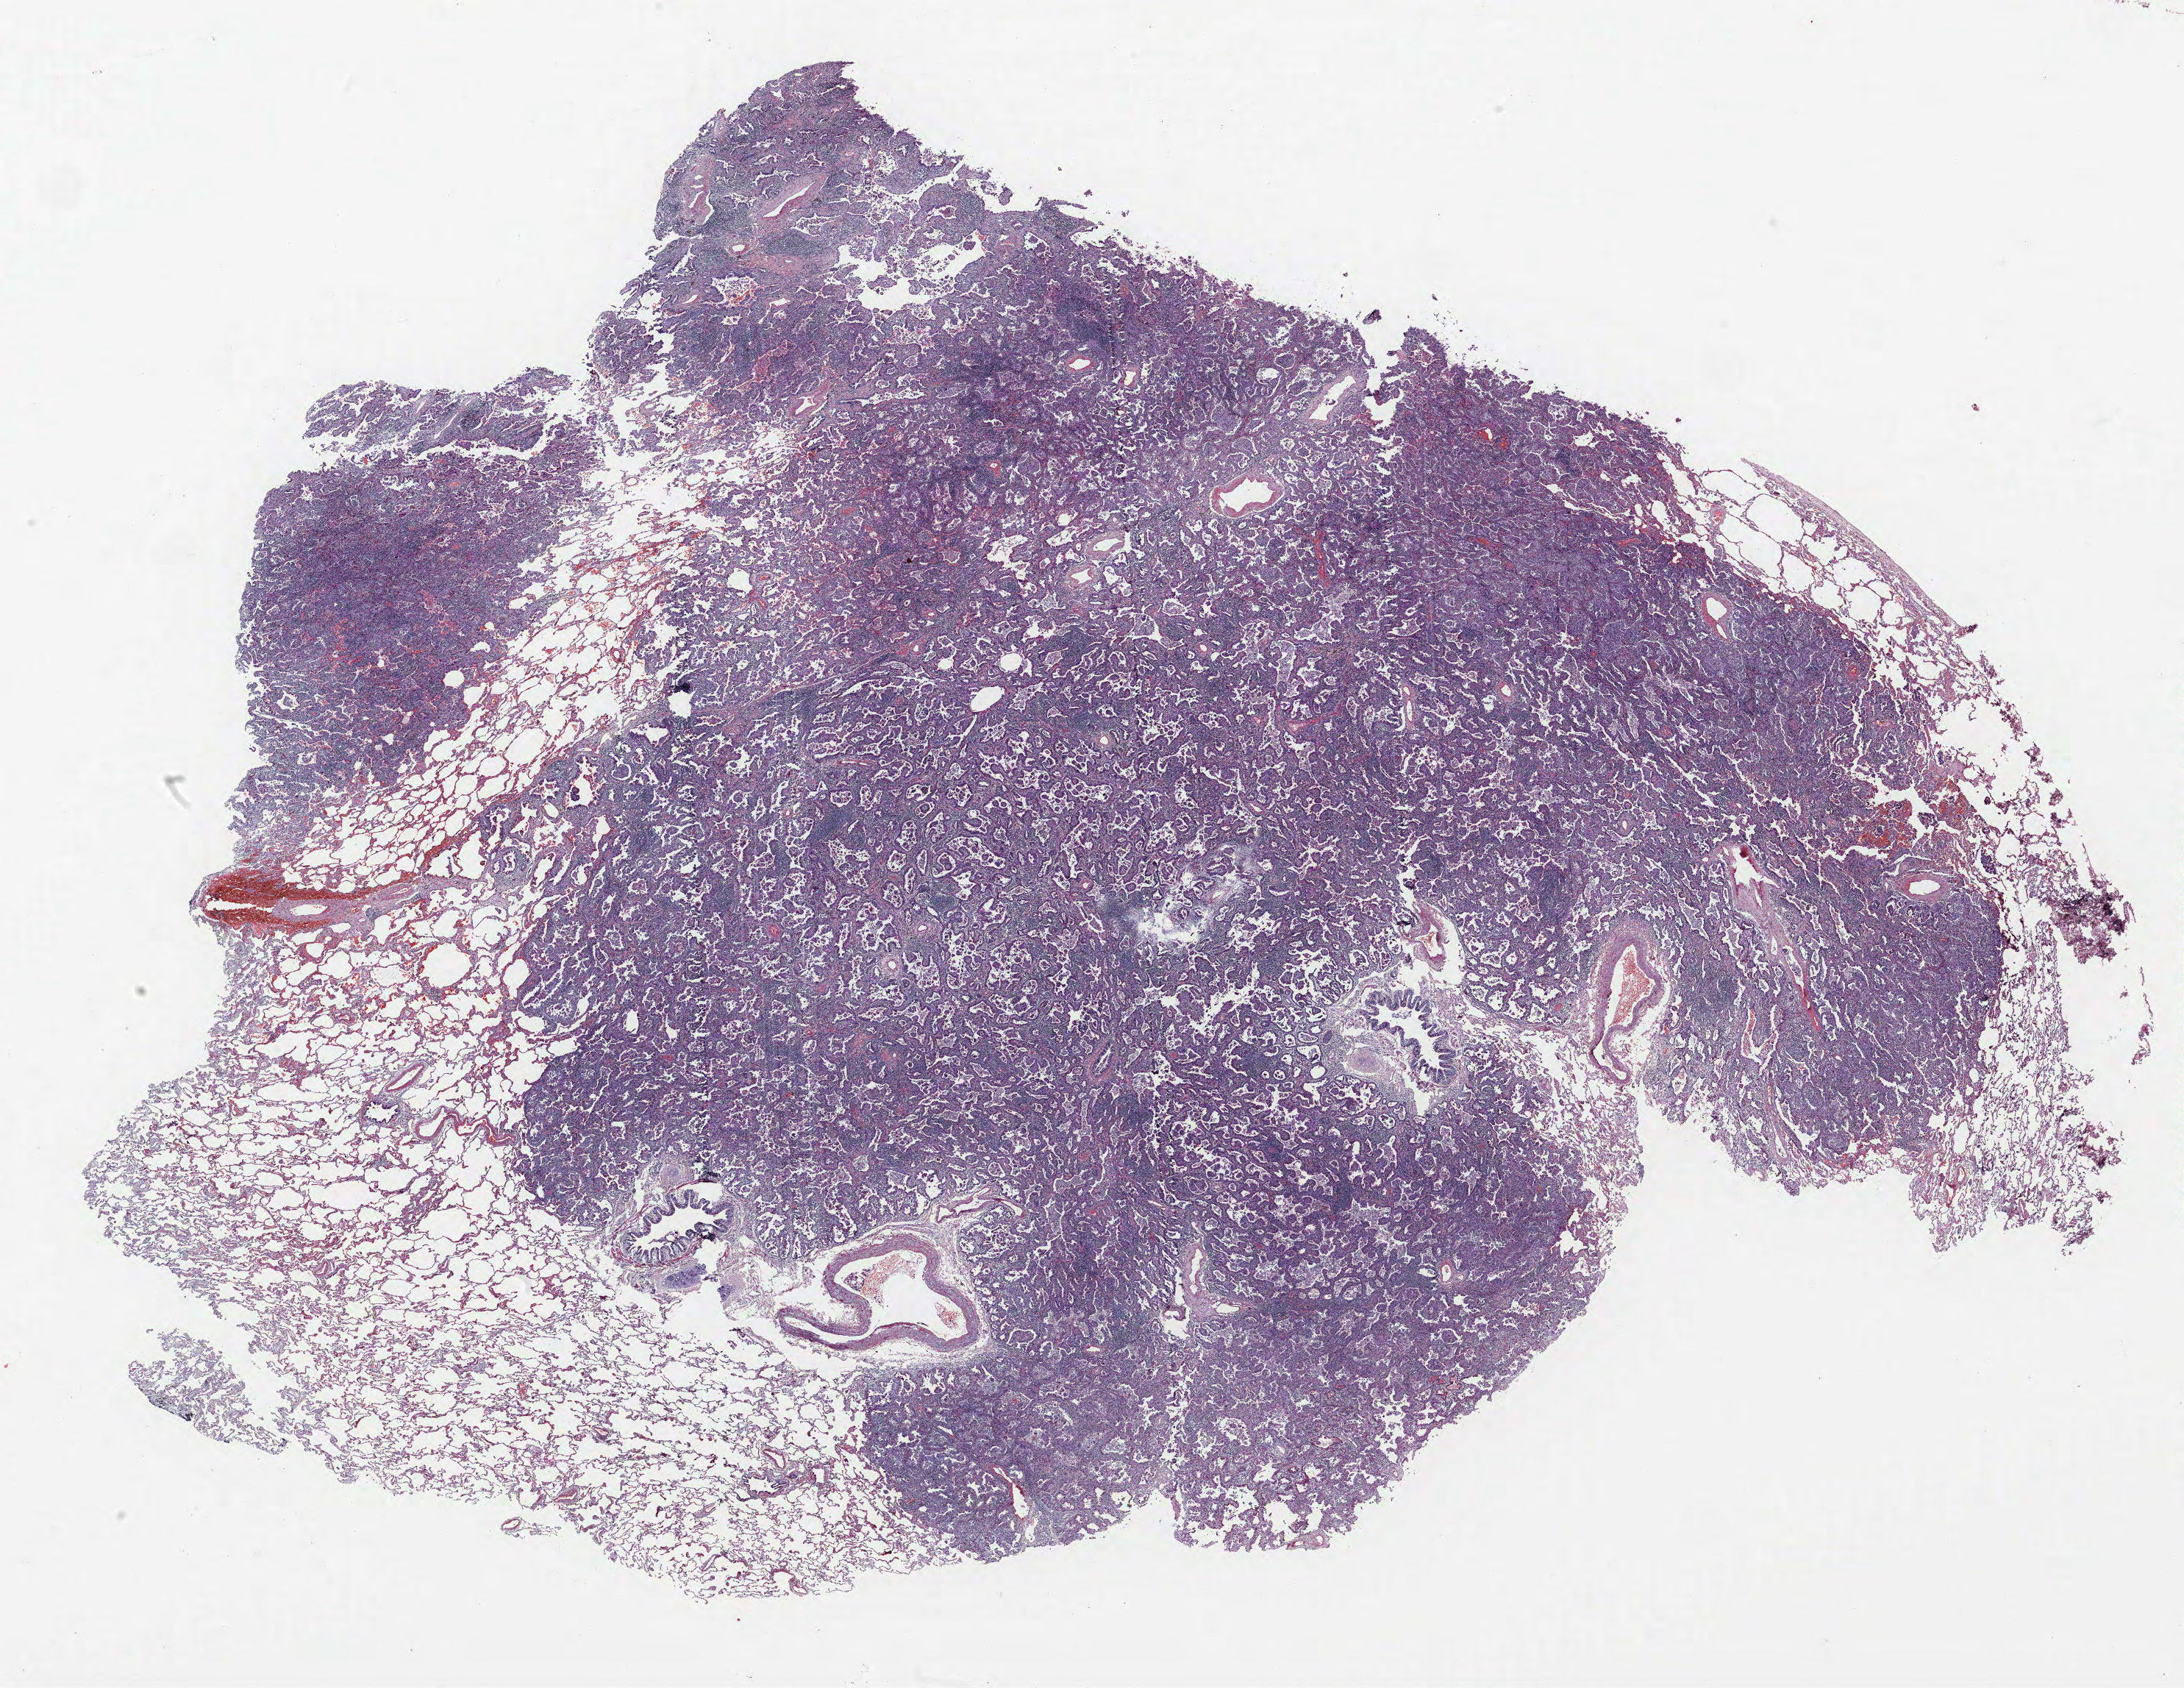
Whole-slide histology image, Hematoxylin and eosin (H&E) stained — low-resolution overview of the scanned area, about 23.8 x 18.4 mm (slide scanned at 40x), formalin-fixed paraffin-embedded (FFPE) section, lung. Female, age 57 at enrolment. Former smoker at enrolment. Grade: well differentiated (G1).
* stage (AJCC 6th edition): IA
* primary tumour location (clinical record): right middle lobe
* tumour size (pathology): 21 mm
* participant's lung-cancer diagnosis: Adenocarcinoma, NOS